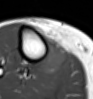
MRI of an extremity soft-tissue mass, one axial slice. Slice 29 of 54 in the series (ordered by position). MR volume resampled by the dataset authors to the PET/CT grid (not the native acquisition matrix). 93 × 99 image matrix. Female patient. Case-level facts recorded for this patient, not image findings: histological type: undifferentiated – high grade; grade: high; site of the primary tumour: right thigh.
Outlined on this slice (expert contour drawn on MRI and transferred to this co-registered scan by the dataset authors):
- gross tumour volume (mass): bounding box [x1, y1, x2, y2] px = [38, 41, 67, 74]